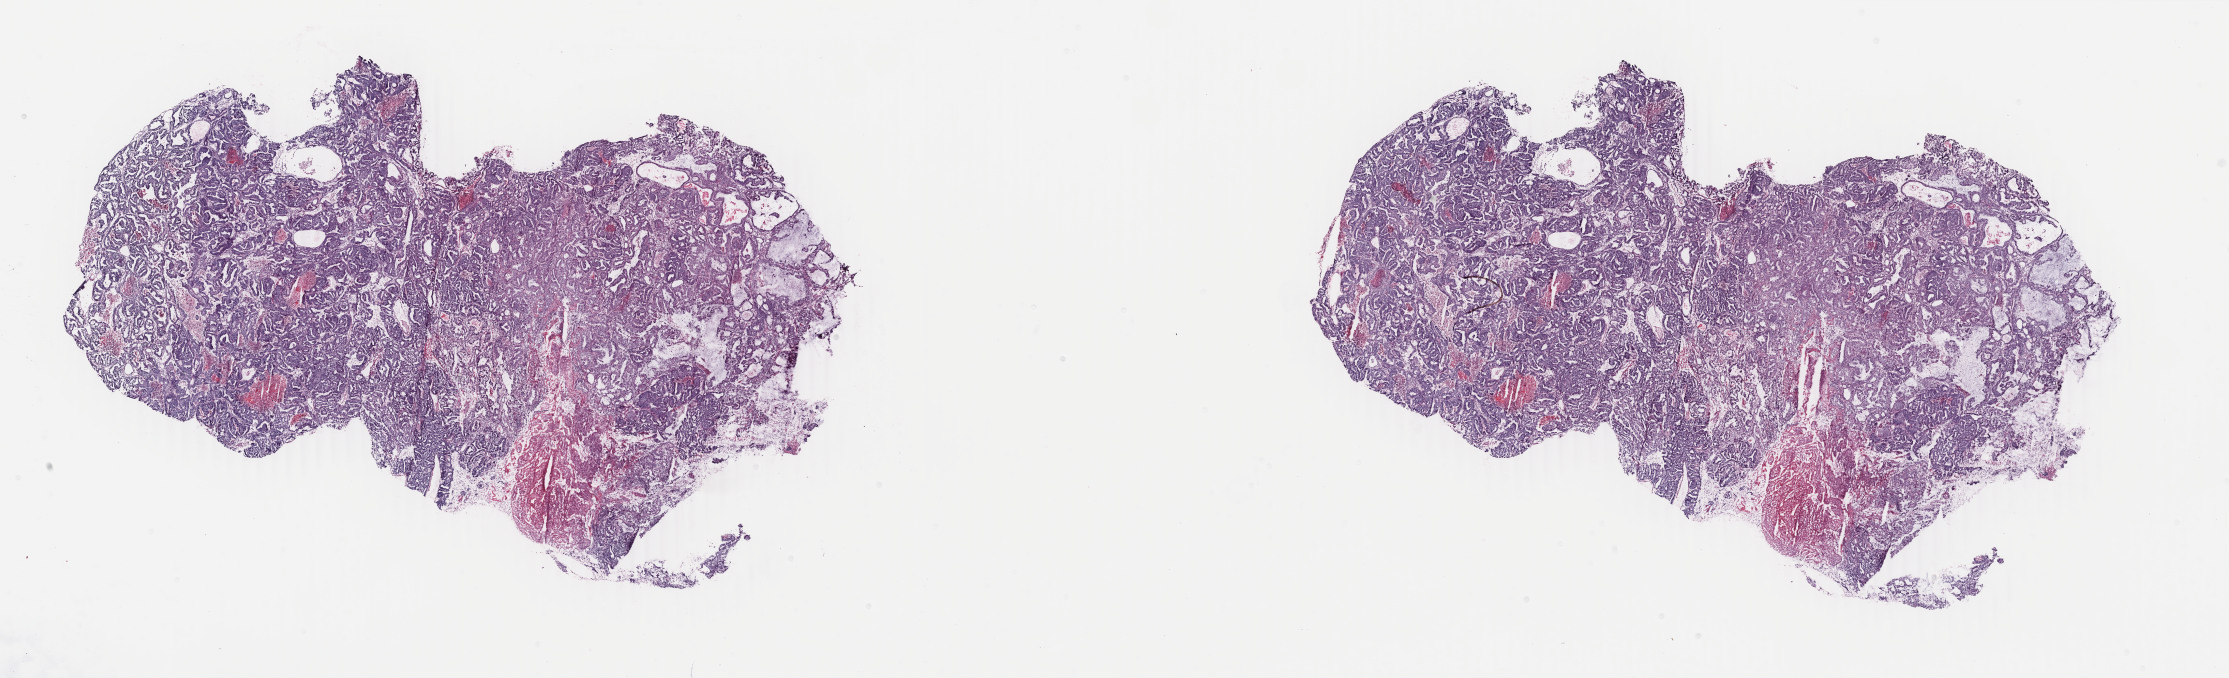
Whole-slide histology image, H&E, a low-resolution overview of the entire scanned area, about 35.5 x 10.8 mm (from a 40x scan); frozen section from the top of the tissue portion; sample: primary tumour, uterus. Patient: female, age at initial diagnosis 71 years. Histologic grade: G1 (well differentiated). Slide review estimates, as recorded: tumour cells 79%, tumour nuclei 90%, normal cells 0%, stromal cells 3%, necrosis 18%. Inflammatory infiltration, as recorded: lymphocyte infiltration 4%, monocyte infiltration 1%, neutrophil infiltration 2%.
Diagnosis: Endometrioid adenocarcinoma, NOS (endometrium). FIGO stage: IA.